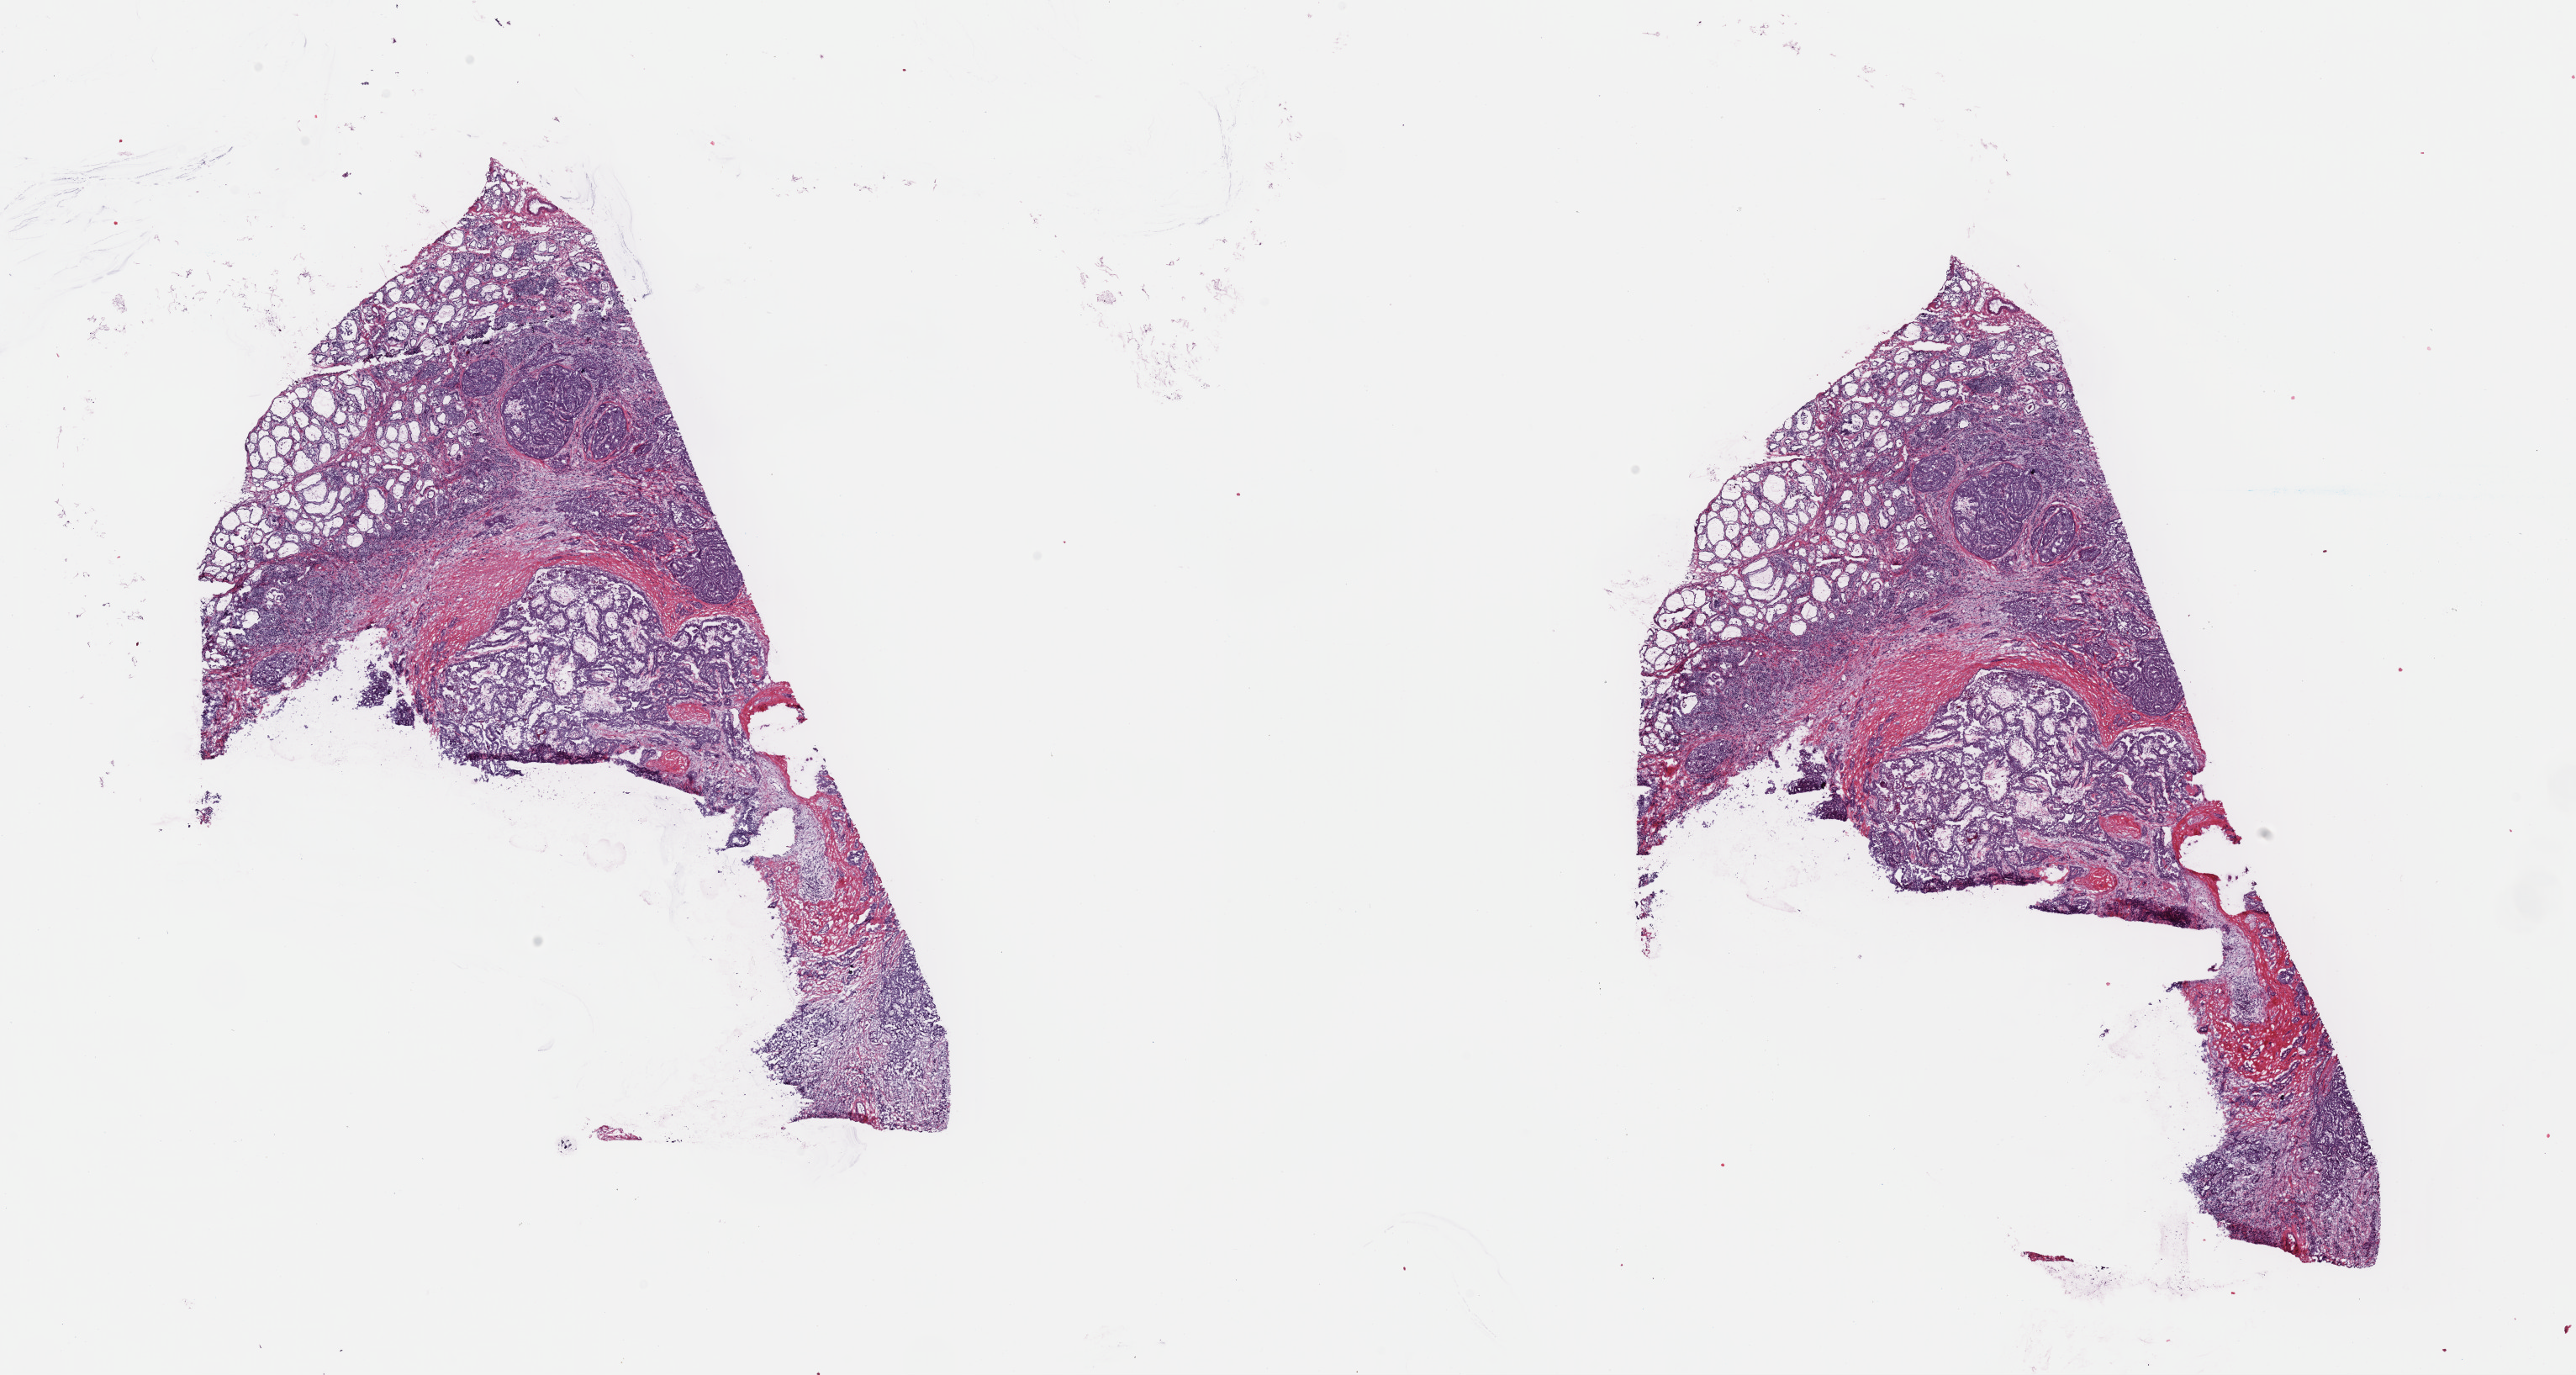
Whole-slide histology image, H&E-stained, low-resolution overview of the scanned area, about 24.2 x 12.9 mm; frozen section; primary tumour sample from the thyroid. Female patient; age at initial diagnosis 52 years. Slide review estimates, as recorded: tumour cells 40%, tumour nuclei 70%, normal cells 30%, stromal cells 30%, necrosis 0%. Infiltration values recorded for this section: lymphocyte infiltration 20%, monocyte infiltration 0%, neutrophil infiltration 0%.
- laterality: right
- diagnosis: Papillary adenocarcinoma, NOS (thyroid gland)
- AJCC pathologic stage: I